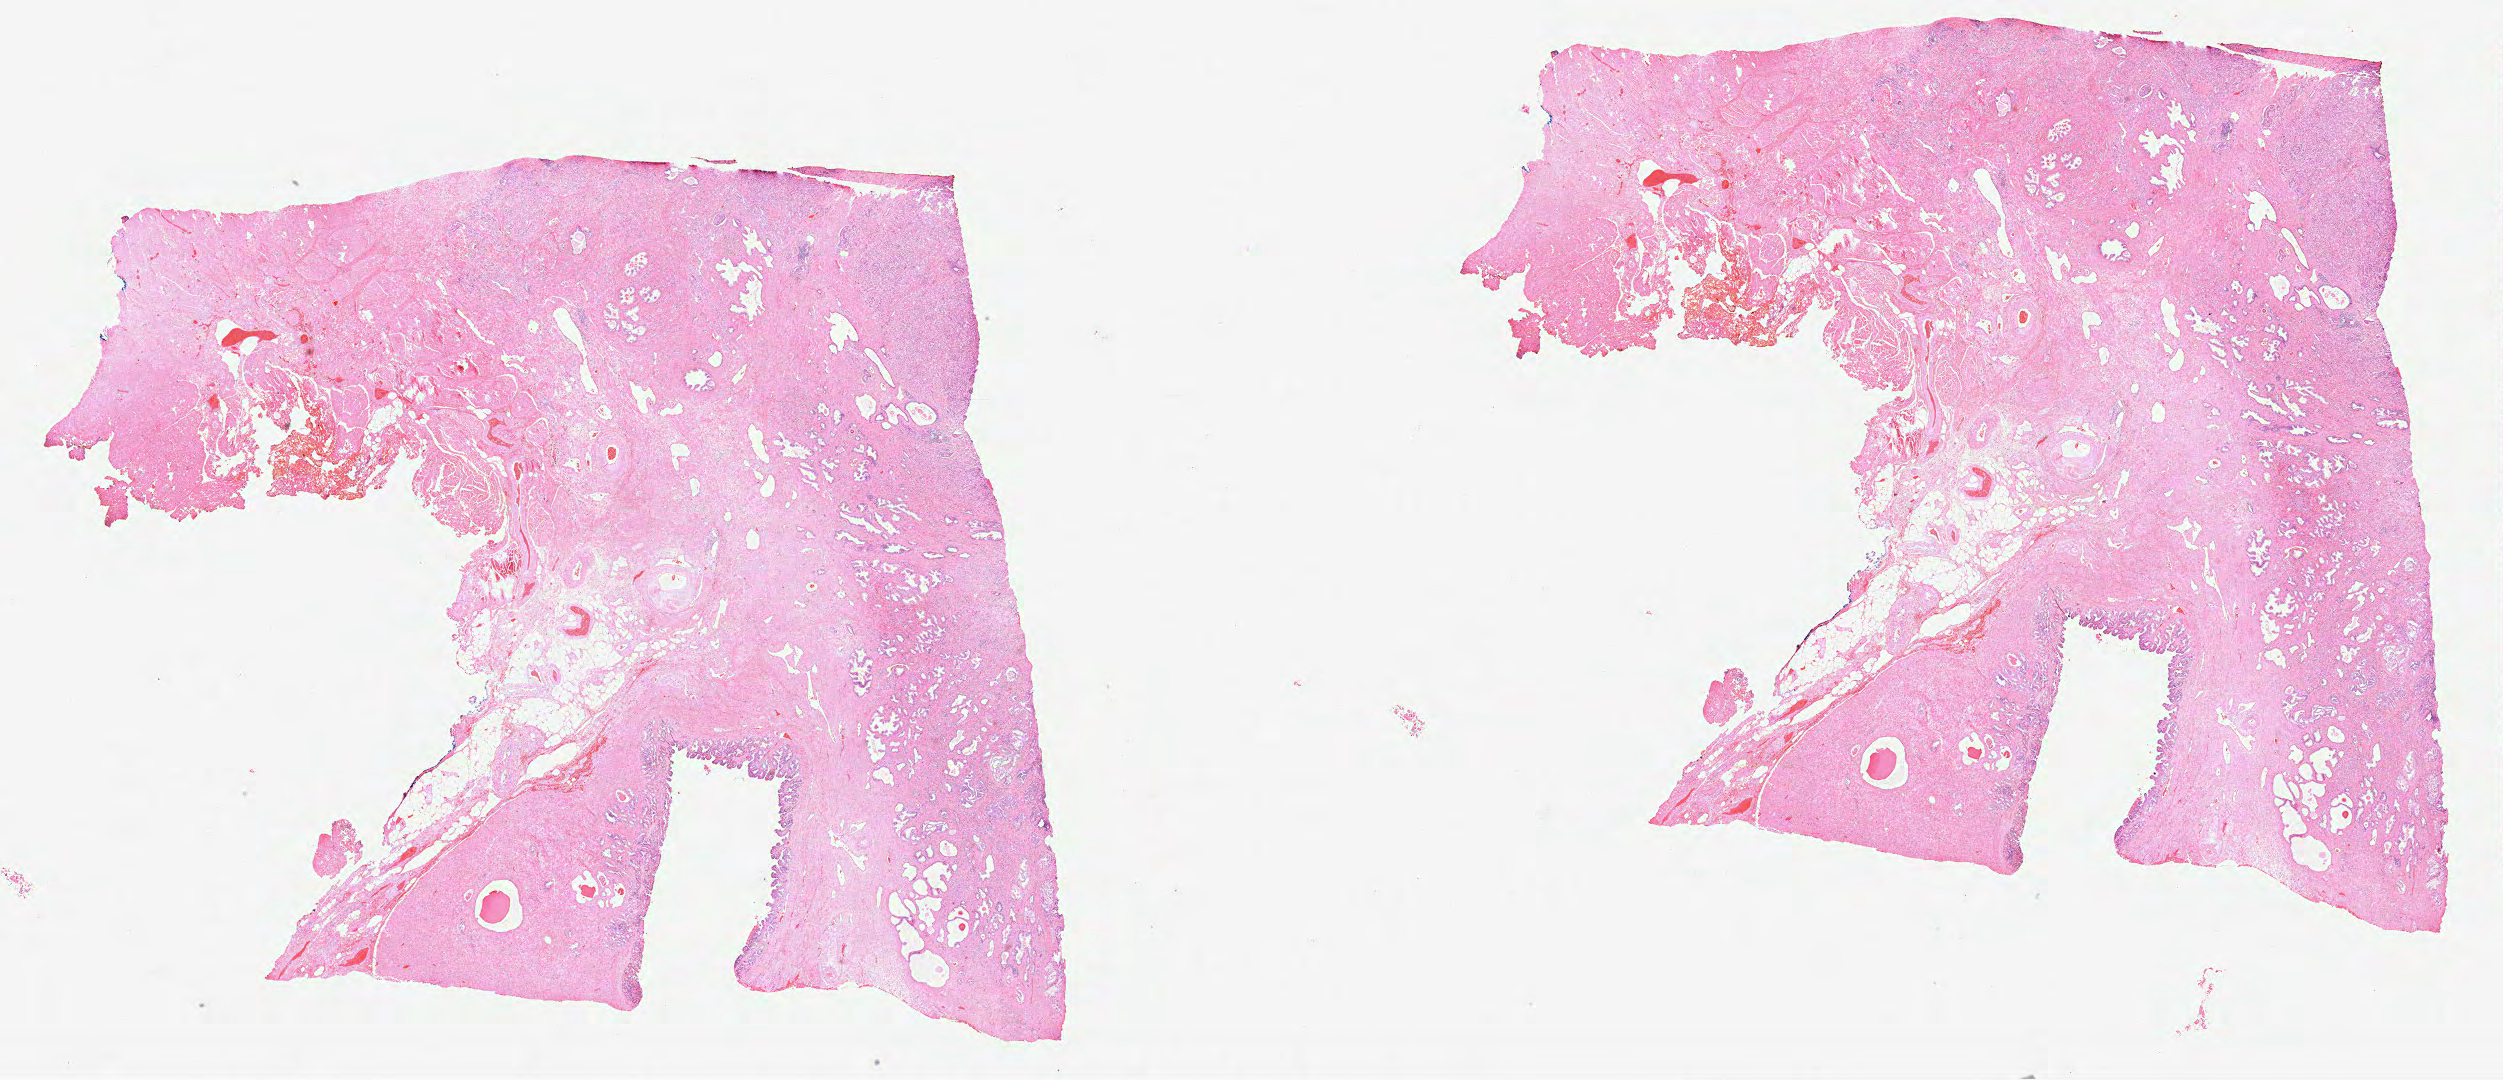
Whole-slide histology image, H&E-stained — low-resolution overview of the scanned area, about 40.4 x 17.4 mm (slide scanned at 40x), formalin-fixed paraffin-embedded (FFPE) diagnostic section, sample: primary tumour, prostate. Male patient; age at initial diagnosis 64 years.
Histologic diagnosis: Acinar cell carcinoma.